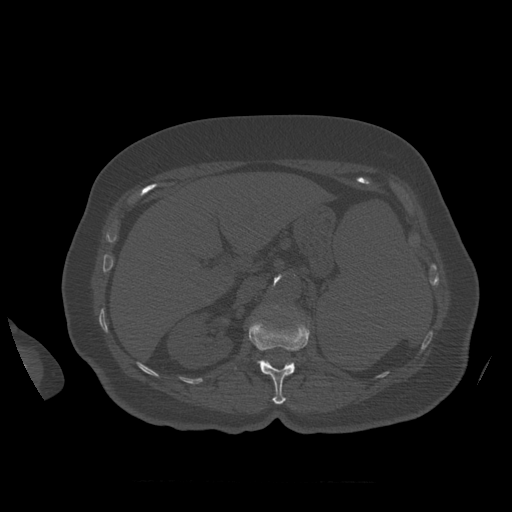
CT including the spine, one axial slice; slice 273 of 399 in the series (ordered by position); reconstruction kernel STANDARD; 120 kVp; bone window (W 1800 / L 400 HU); 1.25 mm slice thickness; 512 × 512 image matrix, field of view 404 × 404 mm. Patient age 81 years. Case-level facts recorded for this patient, not image findings: primary cancer: renal; vertebrae with lytic lesions (as recorded): L1.
Outlined on this slice (semi-automatic segmentation, software-assisted and operator-edited):
- L1 vertebra: box from (x=249, y=320) to (x=310, y=405) px
- L2 vertebra: (x=272, y=306)–(x=277, y=309)